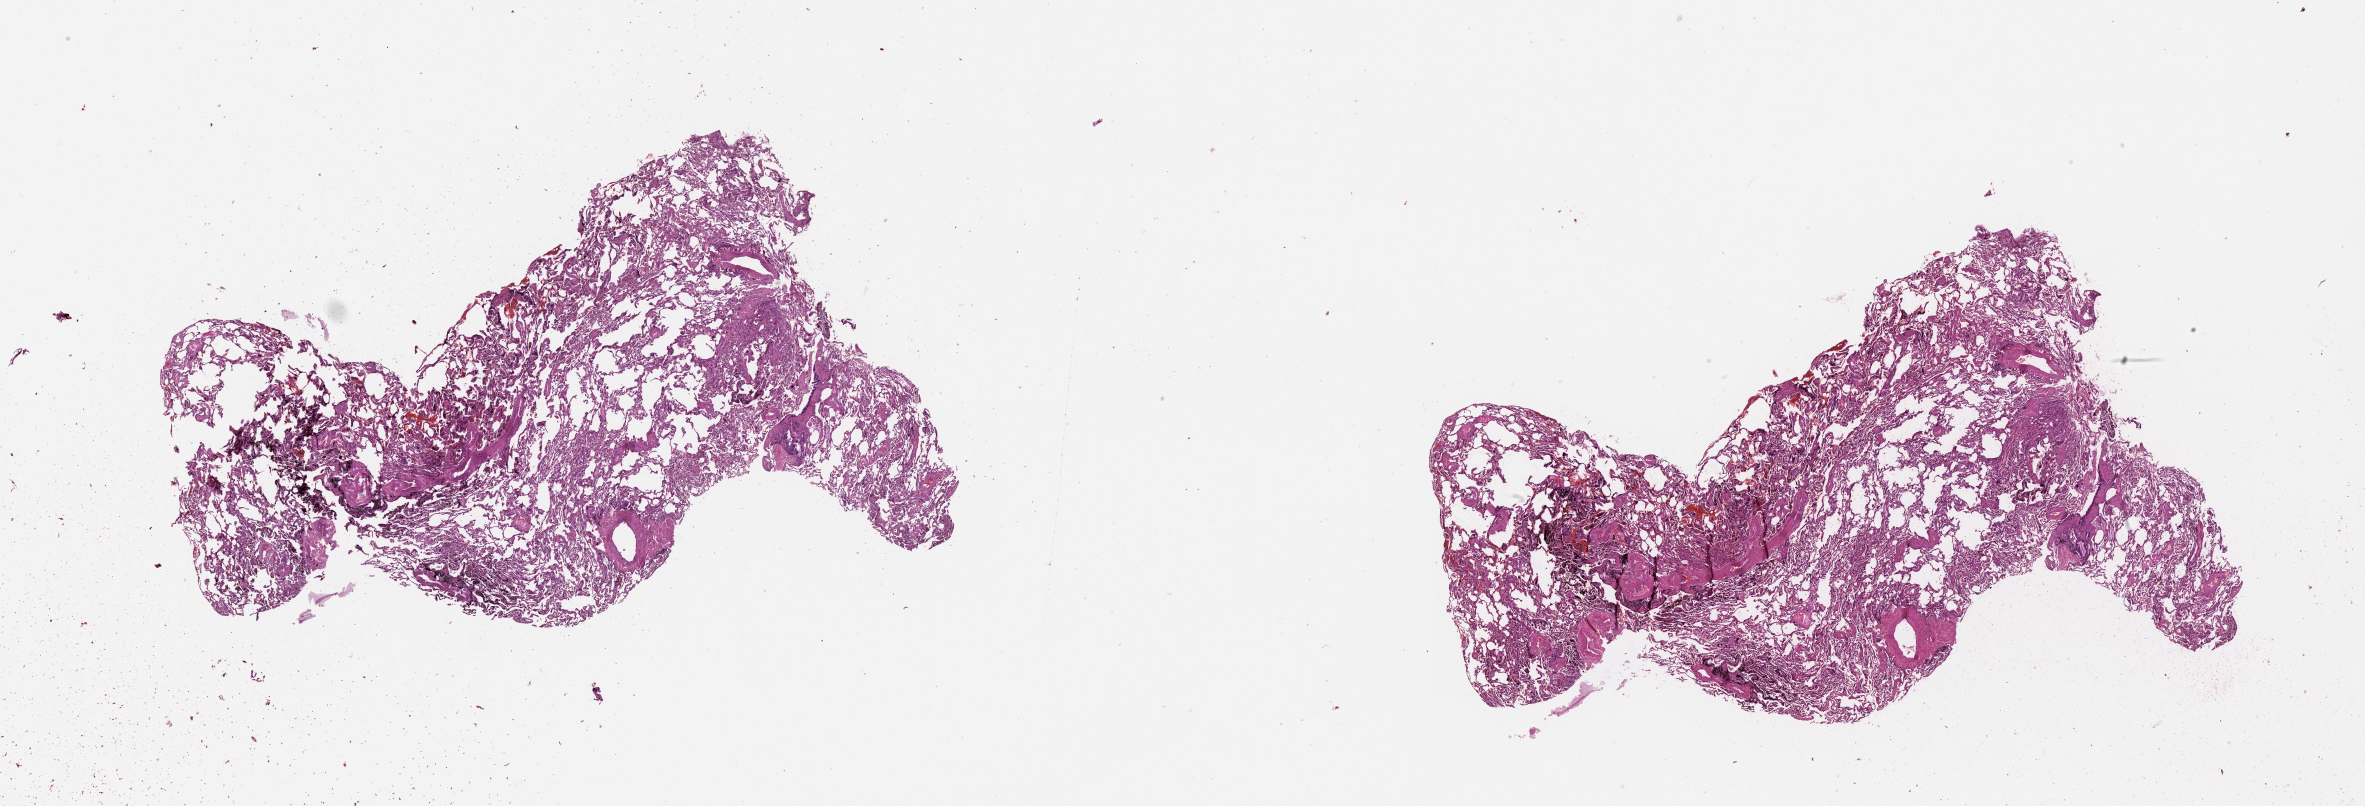
Hematoxylin and eosin (H&E) stained whole-slide image — shown as a low-resolution overview of the whole scanned area (about 38.1 x 13.0 mm). Lung, normal (non-tumour) tissue. Male, 59 y/o.
This section: normal (non-tumour) tissue from the same patient. Patient diagnosis (cohort enrolment): squamous cell carcinoma (lung).